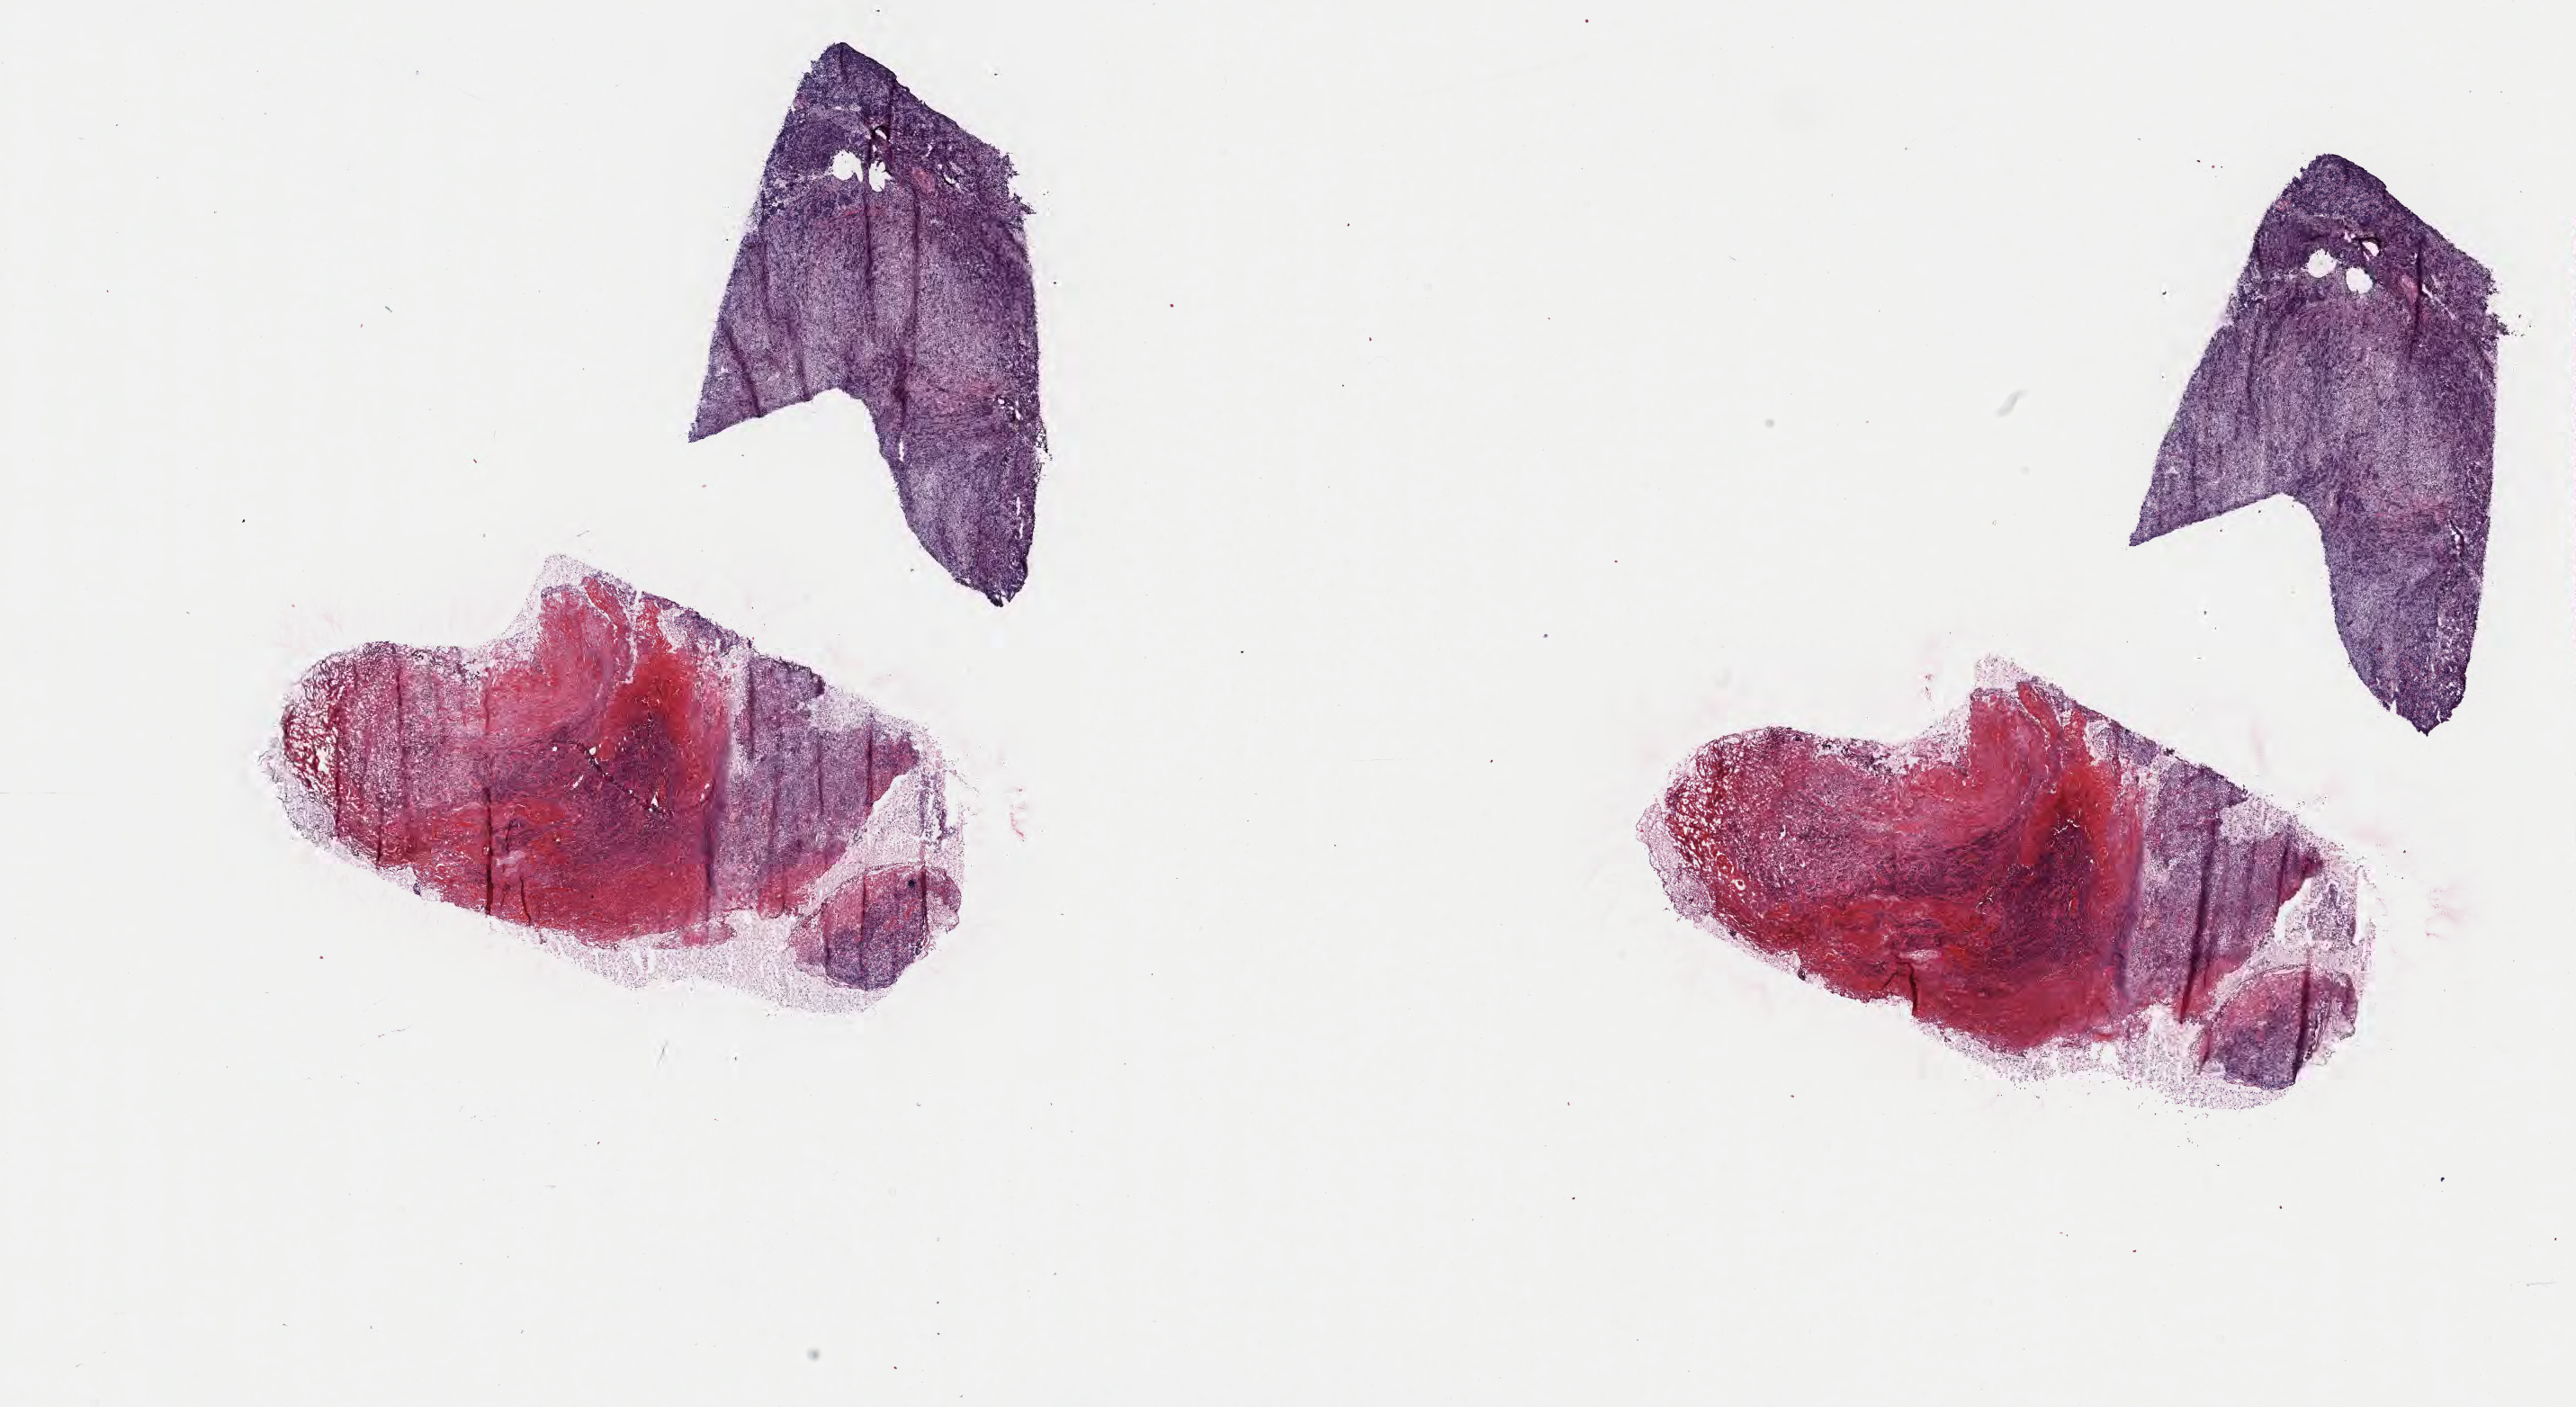
Digitized hematoxylin and eosin (H&E)-stained section, low-resolution overview of the scanned area, about 23.2 x 12.6 mm, cryosection, primary tumor, anatomic site: mandible. Female, age 8 years at initial diagnosis. Pathologist review of this section (percent, as recorded): tumor cells 60%, tumor nuclei 80%, stromal cells 10%, necrosis 30%, normal cells 0%. Infiltration values recorded for this section: lymphocyte infiltration 30%, monocyte infiltration 30%, neutrophil infiltration 10%.
Ann Arbor stage (patient): Stage II. Histologic diagnosis: Burkitt lymphoma, NOS.